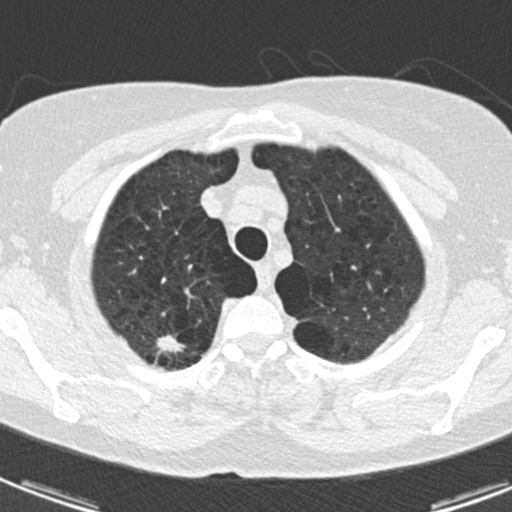
Chest CT (low-dose screening protocol), one axial image, third annual screen, lung window (W 1500 / L -600 HU), 2 mm slice thickness, standard (soft-tissue) reconstruction kernel (B30f), slice 23 of 174 in the series, 512 × 512 image matrix. Female, age 59 years at enrolment.
Lesion marked by an expert reader, bounding box (x1, y1, x2, y2) in pixels: (132, 320, 190, 365). The exam's reader record, not a measurement of the box and not confirmed to be the same lesion: non-calcified nodule or mass ≥4 mm, right upper lobe, 12 × 7 mm, spiculated (stellate) margins, soft tissue attenuation, pre-existing on the prior screen: yes; interval growth: yes. Official screen result: positive, other. Later outcome: lung cancer diagnosed 32 days after this screen — adenocarcinoma, NOS, right upper lobe, poorly differentiated (G3), stage IA (AJCC 6th edition), 20 mm at pathology.